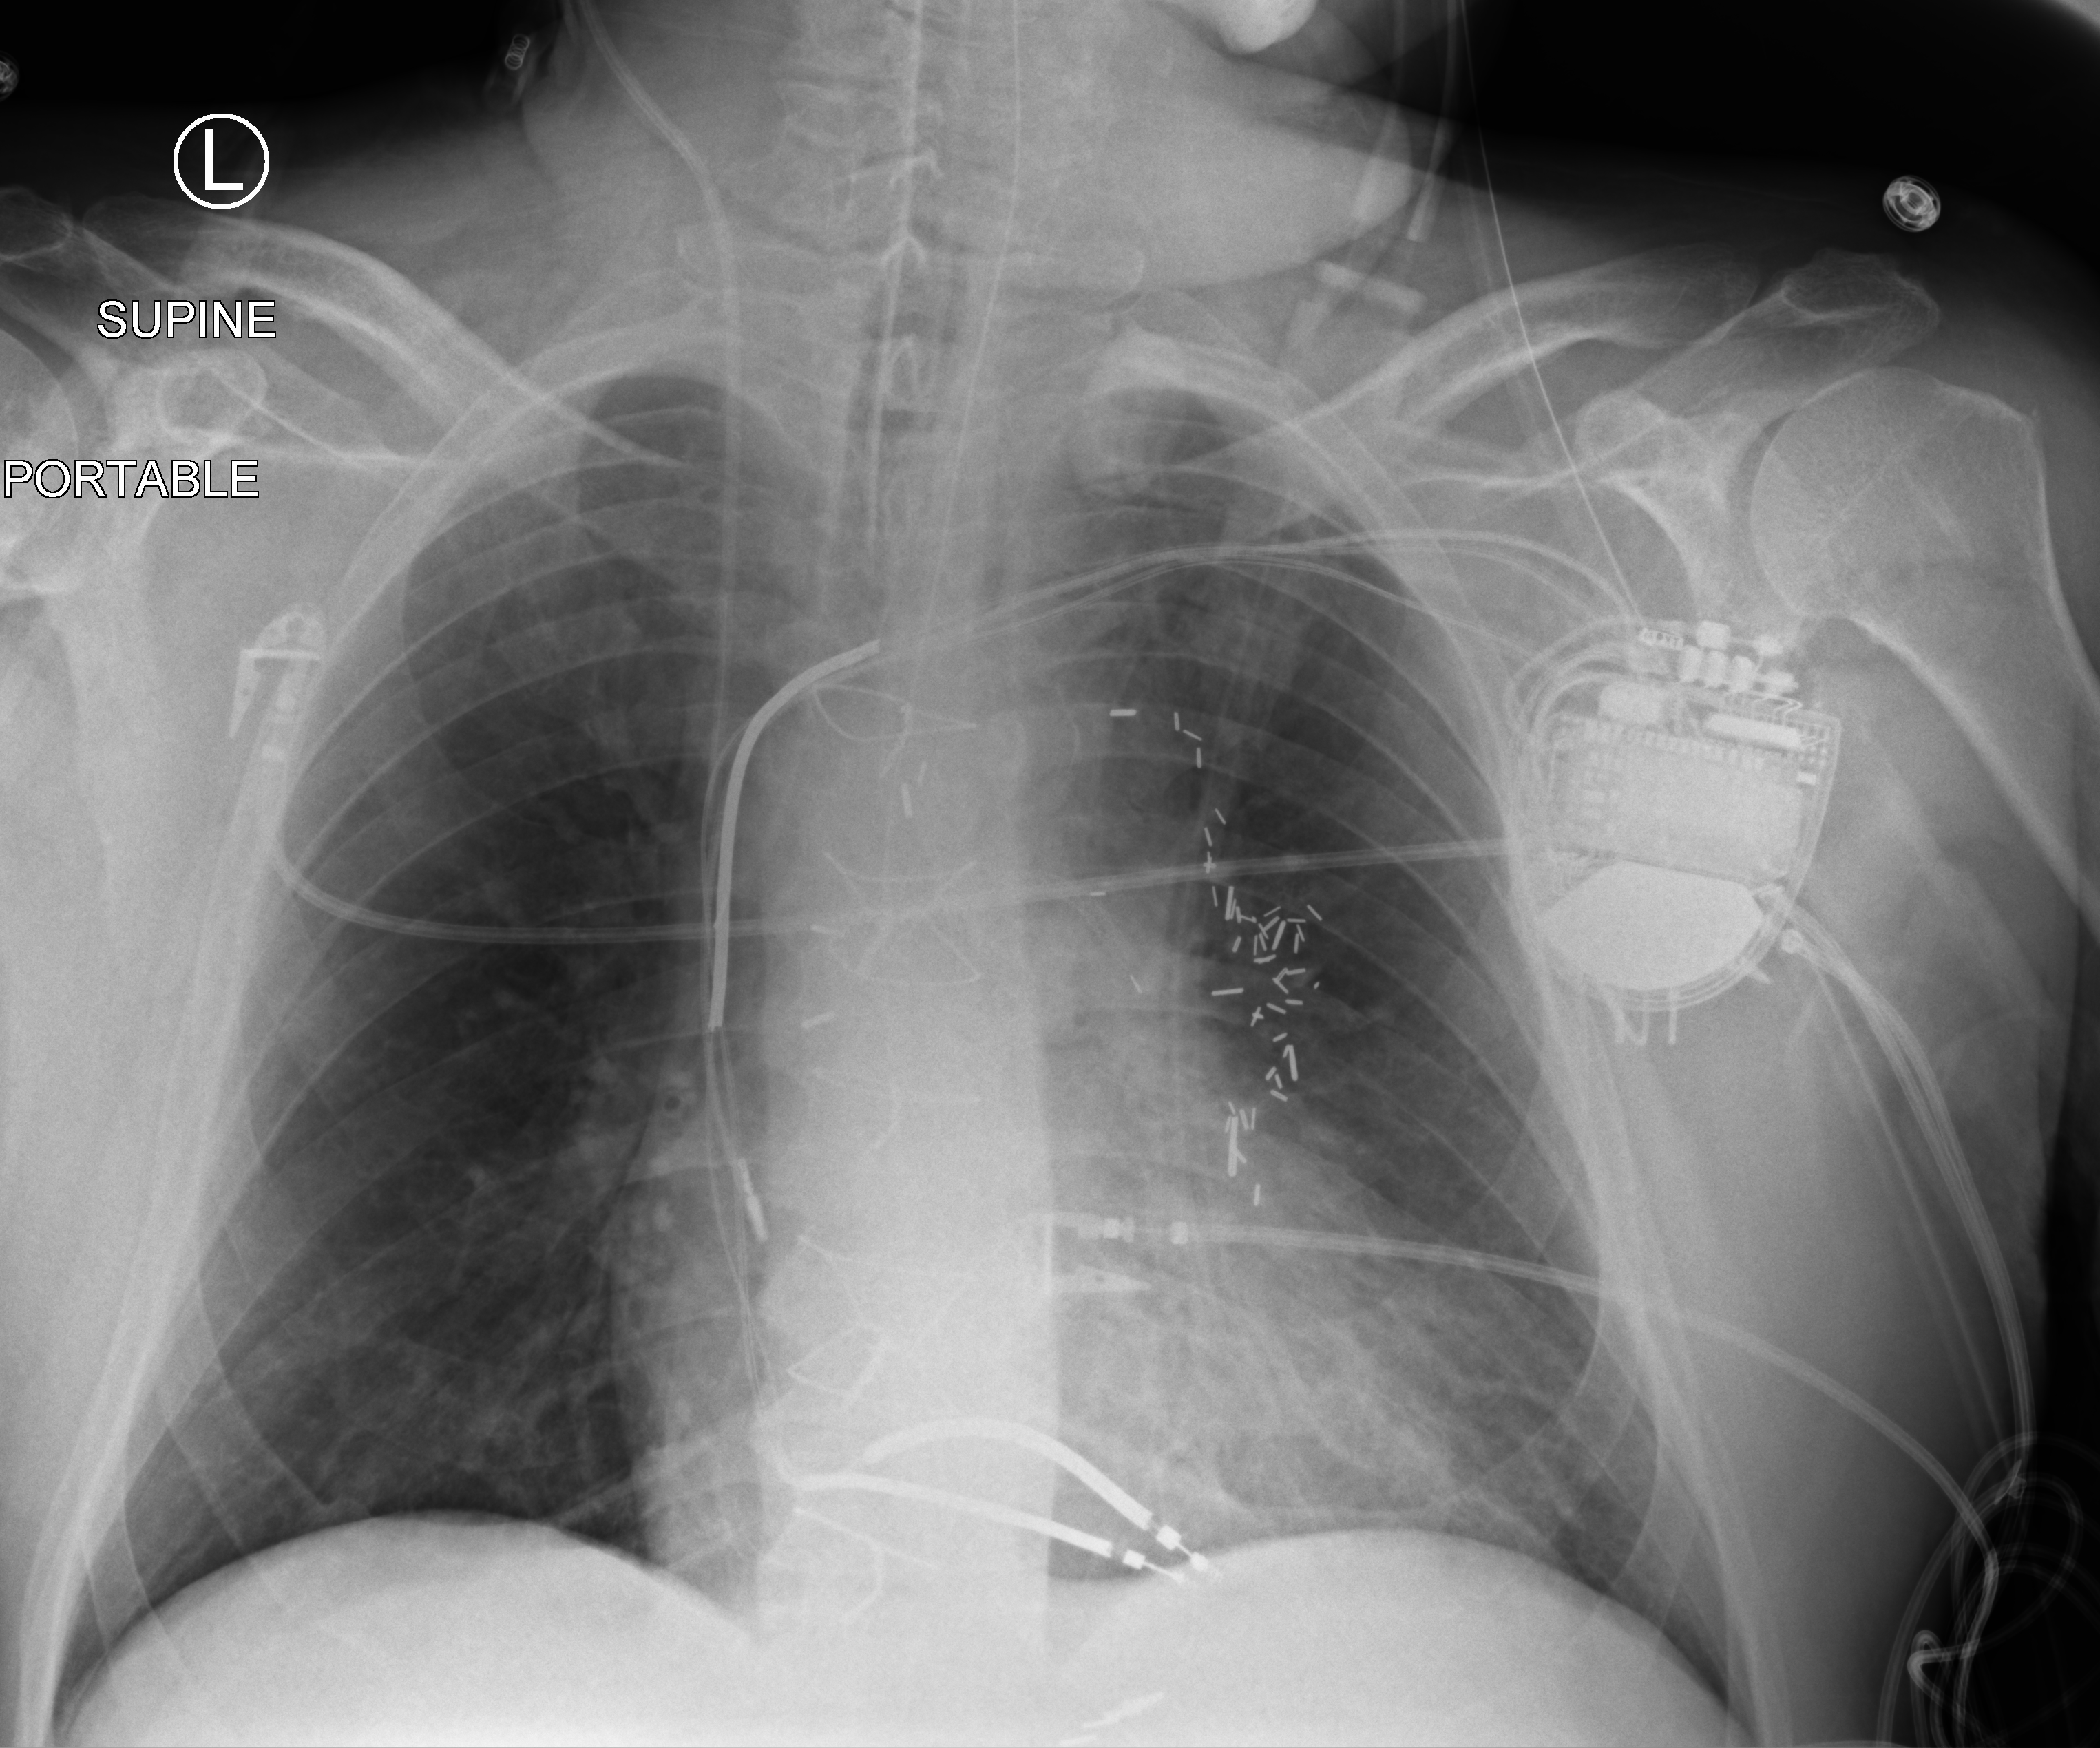
Portable chest radiograph; anteroposterior (AP) projection. Male patient hospitalised with COVID-19, age 60–74 years.
Admission-level facts for this patient (not findings on this image; timing relative to this image not recorded): hypertension (admission record): yes; admitted to intensive care during this hospital stay: yes.